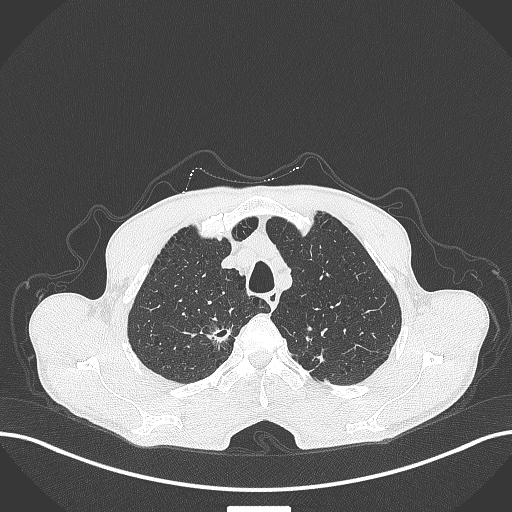
Chest CT, one axial slice. Position 356 of 445 along the scan axis. Reconstruction kernel B70f. 120 kVp. Lung window (W 1500 / L -600 HU). 1 mm slice thickness. 512 × 512 image matrix, field of view 400 × 400 mm. Patient: male, 70 years. From the clinical record (not read from this slice): clinical TNM (as recorded): T1a N0 M0.
Annotated regions visible in this slice (bounding box drawn by a radiologist):
- lung tumour (recorded histology: adenocarcinoma): bounding box [x1, y1, x2, y2] px = [205, 321, 235, 346]